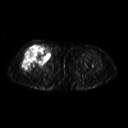
FDG PET of an extremity soft-tissue mass (from a PET/CT study), one axial slice; slice 257 of 311 in the series (ordered by position); 3.27 mm slice thickness; 128 × 128 image matrix, field of view 500 × 500 mm. Female patient, age 57 years. From the clinical record (not read from this slice): histological type: pleiomorphic undifferentiated sarcoma; grade: high; site of the primary tumour: right quadricep.
Outlined on this slice (expert contour drawn on MRI and transferred to this co-registered scan by the dataset authors):
- tumour plus oedema (research contour): box from (x=22, y=45) to (x=50, y=72) px
- tumour (research contour): (x=22, y=45)–(x=50, y=72)